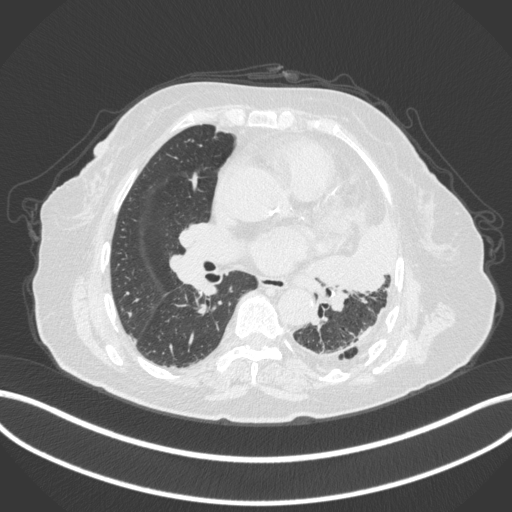
Chest CT, one axial slice. Position 188 of 399 along the scan axis. Reconstruction kernel B31f. Lung window (W 1500 / L -600 HU). 1 mm slice thickness. 512 × 512 image matrix. Female patient, age 75 years. From the clinical record (not read from this slice): clinical TNM (as recorded): T3 N3 M1.
Annotated regions visible in this slice (bounding box drawn by a radiologist):
- lung tumour (recorded histology: adenocarcinoma): bounding box (x1, y1, x2, y2) in pixels: (317, 217, 398, 310)